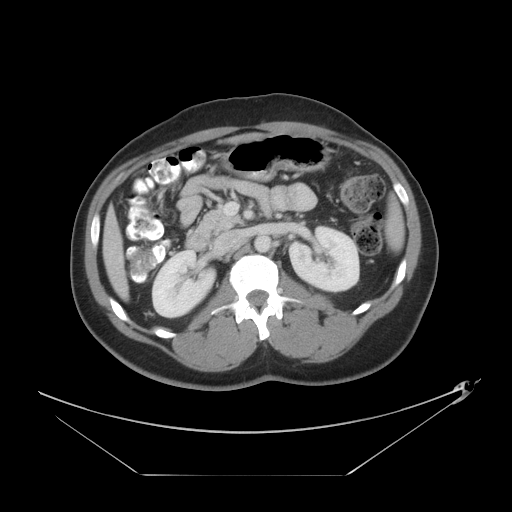
Contrast-enhanced abdominal CT, one axial slice; slice 18 of 44 in the series (ordered by position); reconstruction kernel STANDARD; 120 kVp; intravenous contrast given; soft-tissue window (W 400 / L 40 HU); 512 × 512 image matrix, field of view 466 × 466 mm. Male patient, age 49 years. From the clinical record (not read from this slice): diagnosis: colorectal cancer liver metastases, imaged before liver resection; multiple liver metastases: no; largest metastasis: 8.5 cm; disease in both lobes: yes.
Annotated regions visible in this slice (outlined manually by an expert reader):
- liver: bounding box <103,134,260,299> (left, top, right, bottom; pixels)
- planned liver remnant (the part of the liver to remain after resection): <229,134,259,144>